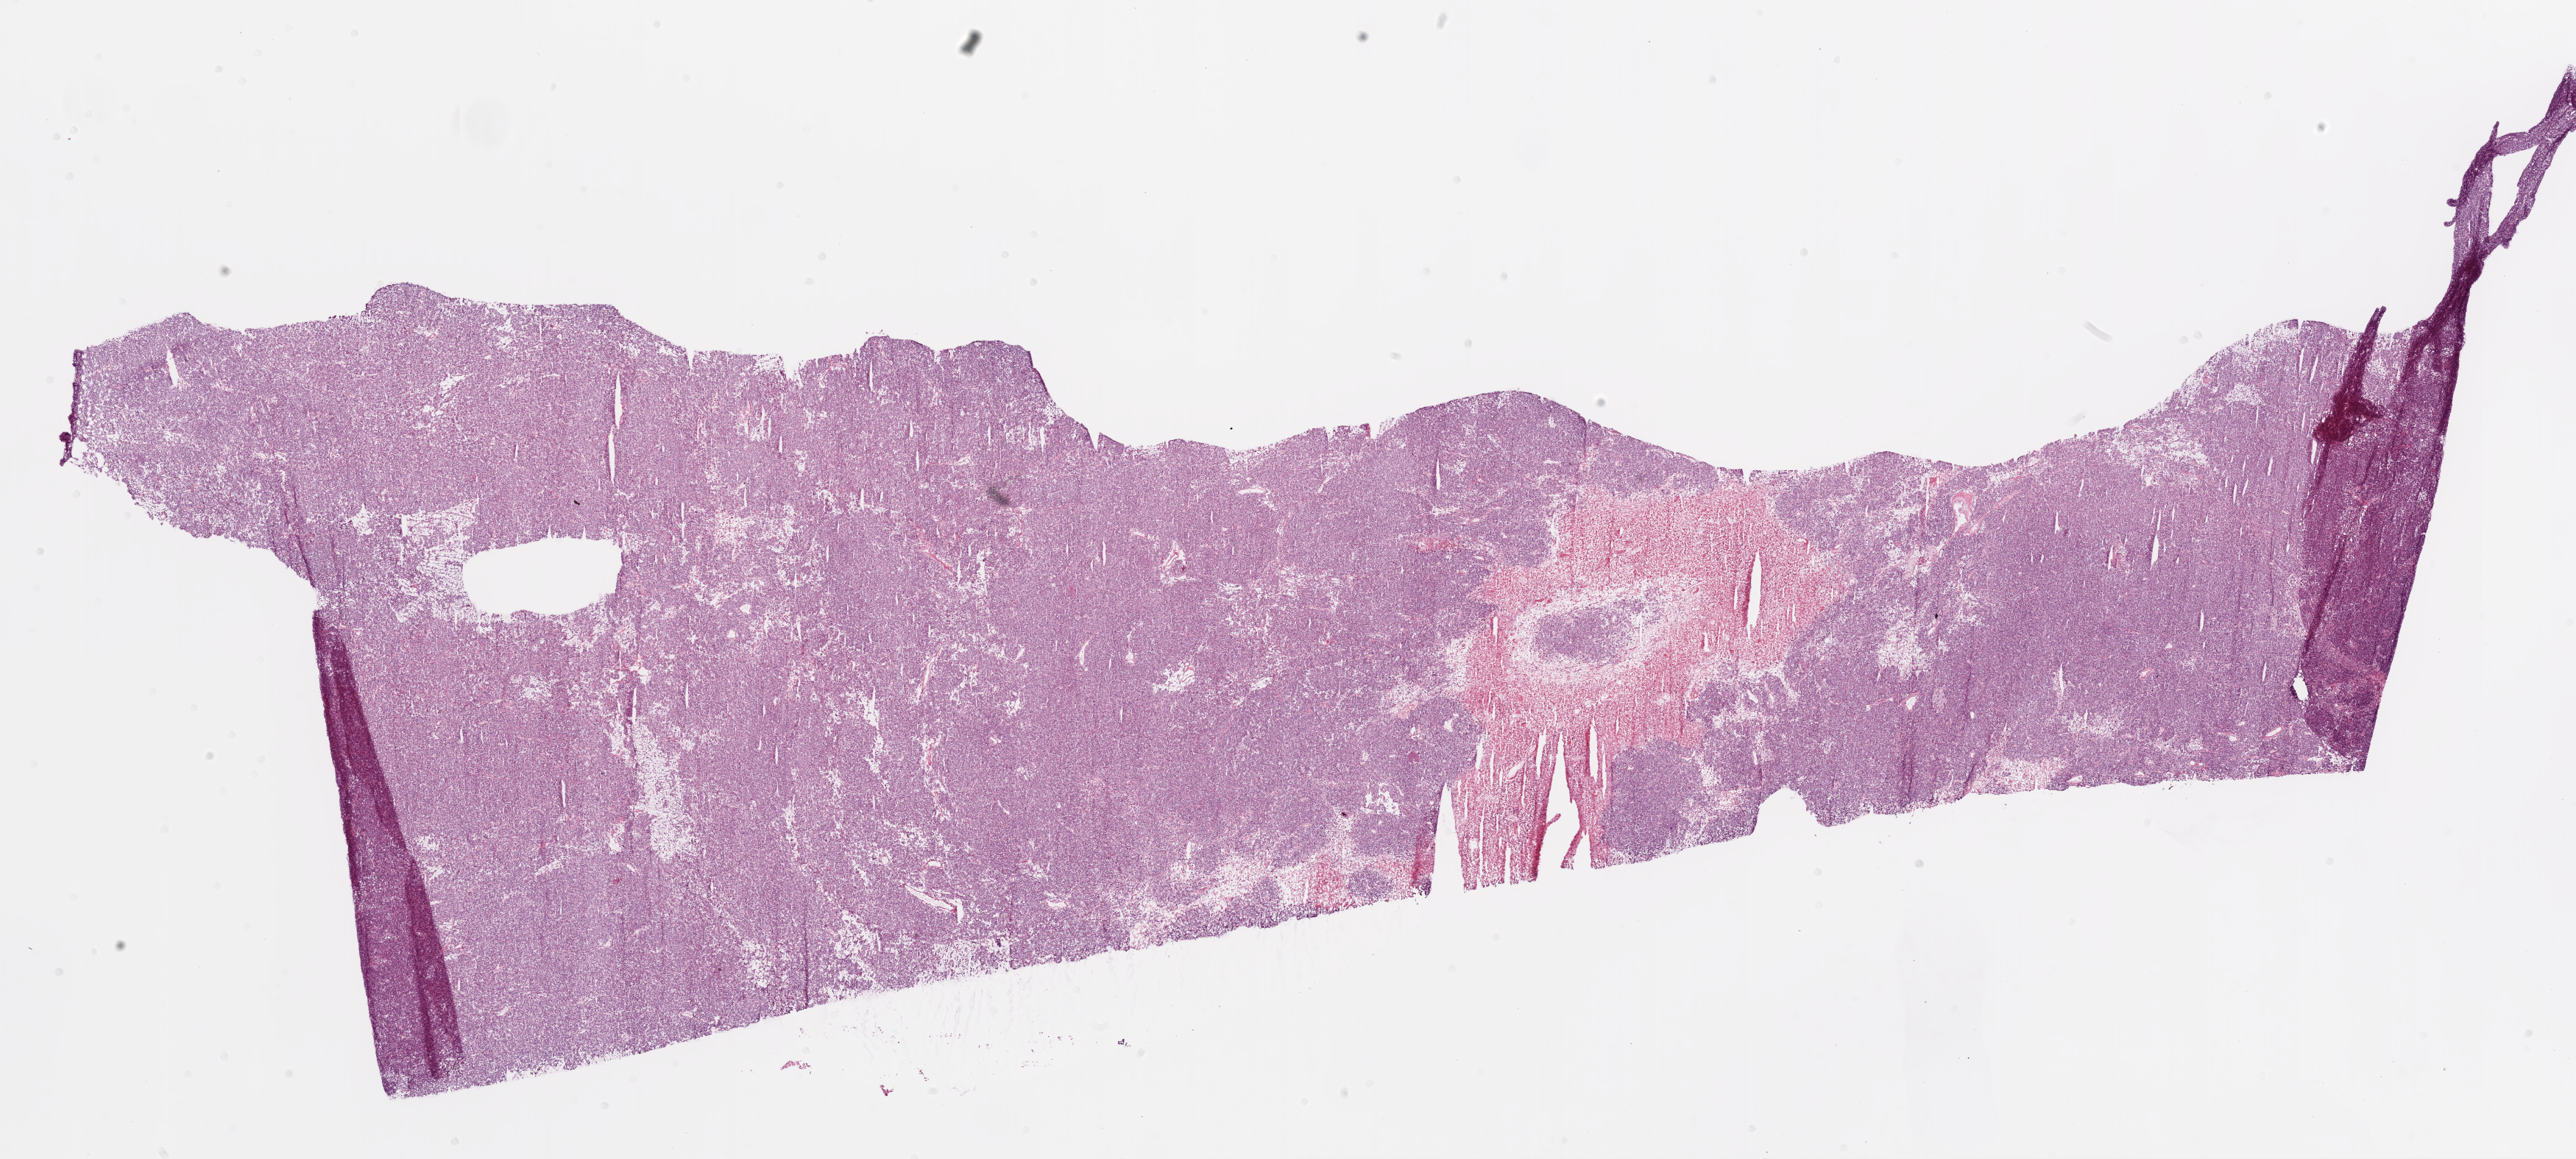
H&E-stained whole-slide image, shown as a low-resolution overview of the whole scanned area (about 28.1 x 12.6 mm, from a 20x scan); frozen section from the top of the tissue portion; ovary, primary tumour sample. Female, age 50 years at initial diagnosis. Histologic grade: G3 (poorly differentiated). Slide review estimates, as recorded: tumour cells 85%, tumour nuclei 99%, normal cells 0%, stromal cells 5%, necrosis 10%.
FIGO stage: IV. Pathologic diagnosis: Serous cystadenocarcinoma, NOS. Laterality: bilateral.